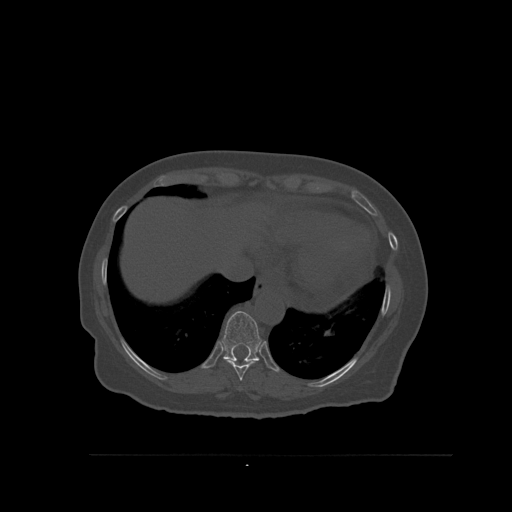
CT including the spine, one axial slice; slice 326 of 527 in the series (ordered by position); bone window (W 1800 / L 400 HU); 1.5 mm slice thickness; 512 × 512 image matrix. Female patient, age 73 years. Case-level facts recorded for this patient, not image findings: primary cancer: breast.
Outlined on this slice (semi-automatic segmentation, software-assisted and operator-edited):
- T10 vertebra: bounding box (x1, y1, x2, y2) in pixels: (222, 311, 262, 361)
- T9 vertebra: (223, 359, 259, 381)